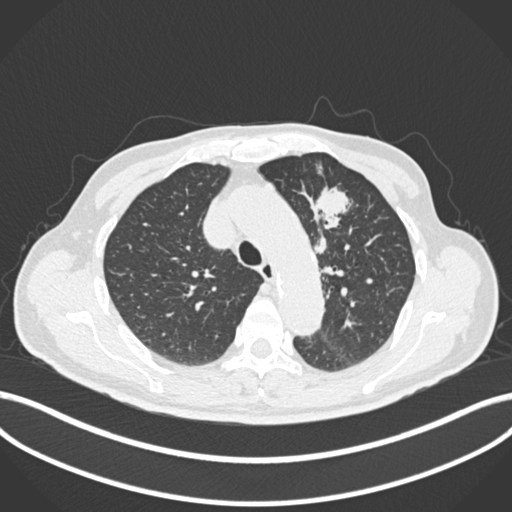
Chest CT, one axial slice; slice 184 of 261 in the series (ordered by position); reconstruction kernel B30f; 120 kVp; lung window (W 1500 / L -600 HU); 1 mm slice thickness; 512 × 512 image matrix, field of view 400 × 400 mm. Male patient, age 74 years. Case-level facts recorded for this patient, not image findings: clinical TNM (as recorded): T2b N0 M1c.
Outlined on this slice (rectangle marked by the reading radiologist):
- lung tumour (recorded histology: adenocarcinoma): bounding box [x1, y1, x2, y2] px = [308, 182, 354, 236]